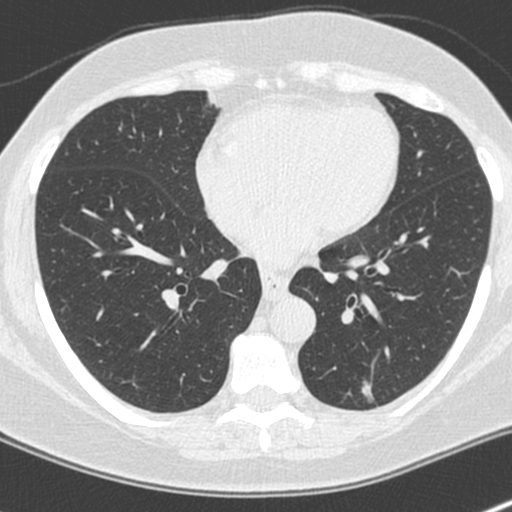
Axial slice from a low-dose chest CT screening exam, baseline screening round, lung window (W 1500 / L -600 HU), 1.3 mm slice thickness, slice 120 of 222 in the series, 512 × 512 image matrix, field of view 300 × 300 mm. Female, age 64 years at enrolment.
Expert reader's lesion annotation, bounding box (x1, y1, x2, y2) in pixels: (346, 371, 390, 418). Screening reader's record for this exam: no non-calcified nodule ≥4 mm recorded. Official screen result: negative screen, no significant abnormalities. Later outcome: lung cancer diagnosed 549 days after this screen — adenocarcinoma, NOS, left lower lobe, poorly differentiated (G3), stage IA (AJCC 6th edition), 8 mm at pathology.